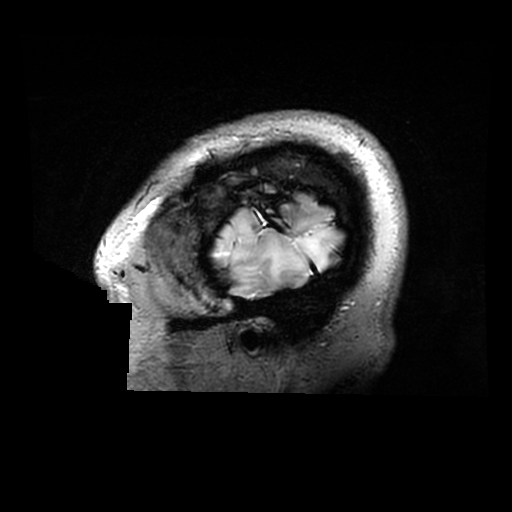
Brain MRI from a brain-tumour surgery series, one sagittal slice. 512 × 512 image matrix, field of view 240 × 240 mm. Case-level facts recorded for this patient, not image findings: histopathology: Astrocytoma; WHO grade: 2; IDH mutation: yes.
Annotated regions visible in this slice (outlined manually by an expert reader):
- tumour: box from (x=214, y=214) to (x=339, y=283) px